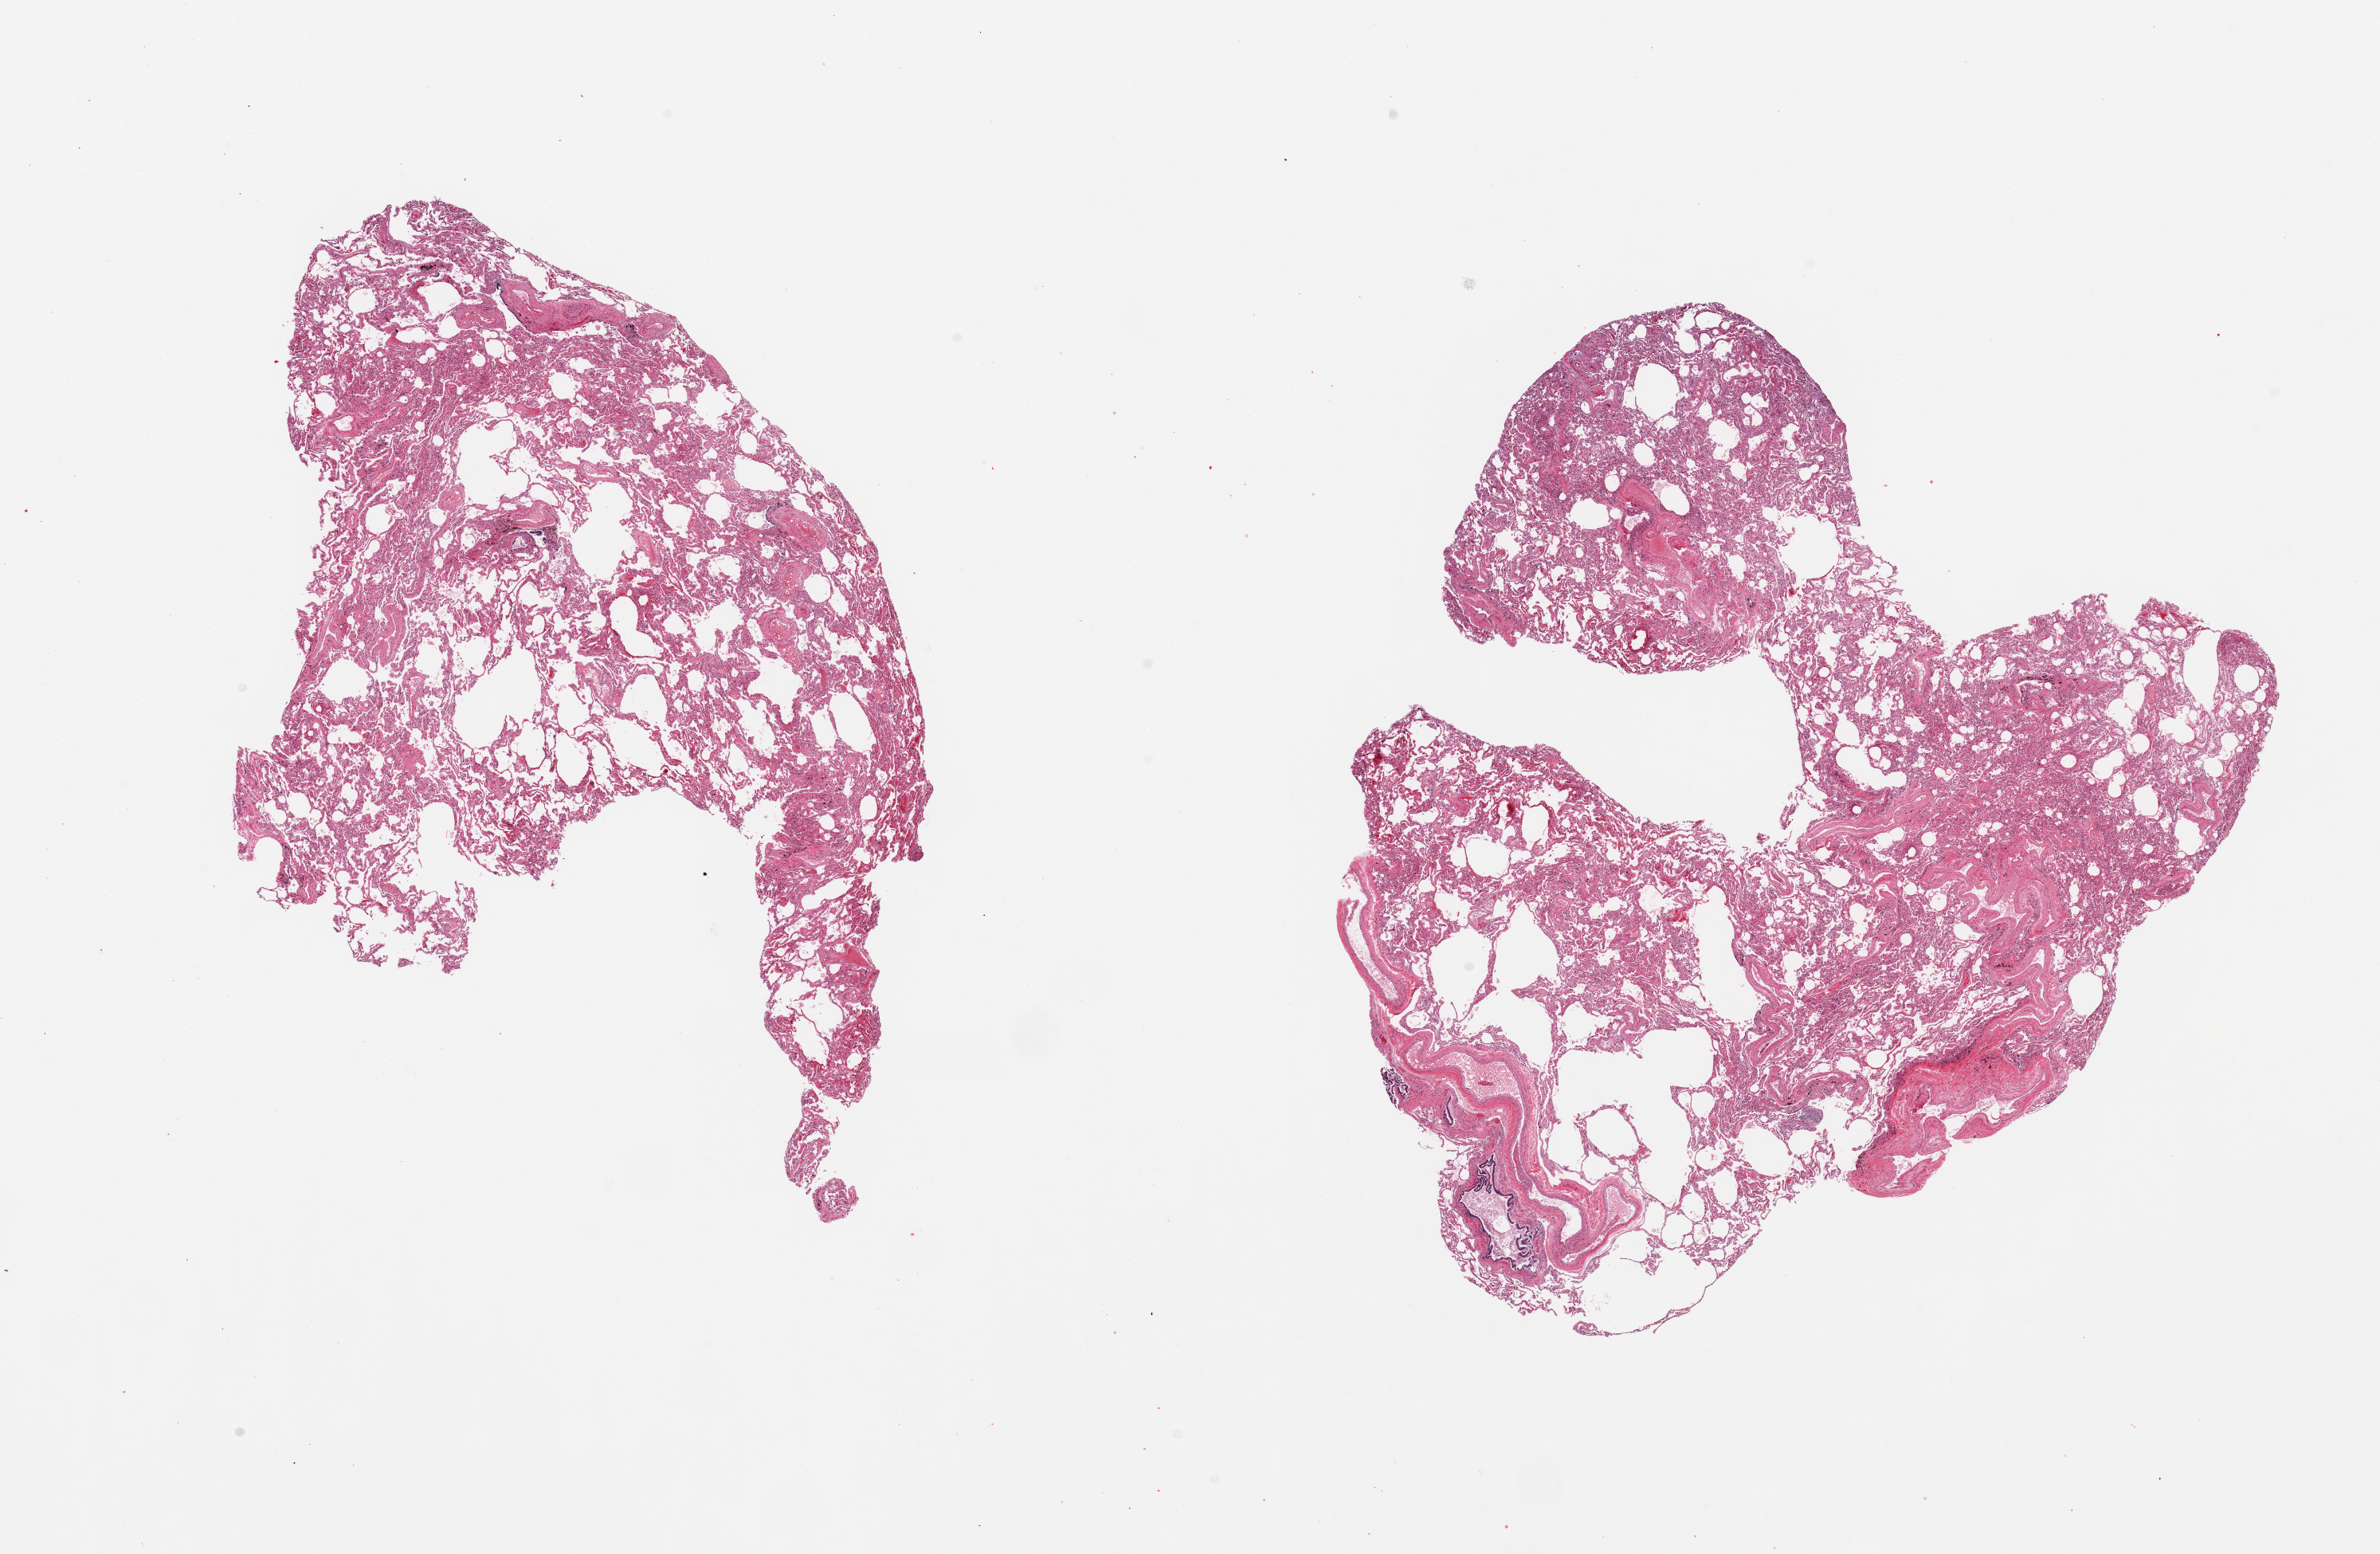
Whole-slide image, haematoxylin and eosin stain — shown as a low-resolution overview of the whole scanned area (about 23.6 x 15.4 mm, acquisition: 20x scan), PAXgene-fixed paraffin-embedded (PFPE) section, sampled site (target tissue): lung, donor tissue sample.
• reviewer comment on this tissue sample: 2 pieces; areas of atelectasis and adjacent widened air spaces; congestion; anthracosis; thick walled vessels